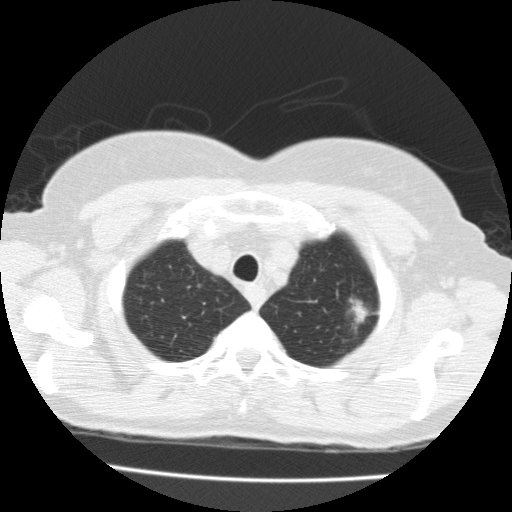
Low-dose screening chest CT, one axial slice; position 160 of 183 along the scan axis; reconstruction kernel FC10; 120 kVp; lung window (W 1500 / L -600 HU); 2 mm slice thickness; 512 × 512 image matrix, field of view 320 × 320 mm.
Annotated regions visible in this slice (expert manual segmentation):
- lesion 1 (tumor, upper lobe of left lung): bounding box (x1, y1, x2, y2) in pixels: (350, 299, 368, 323)